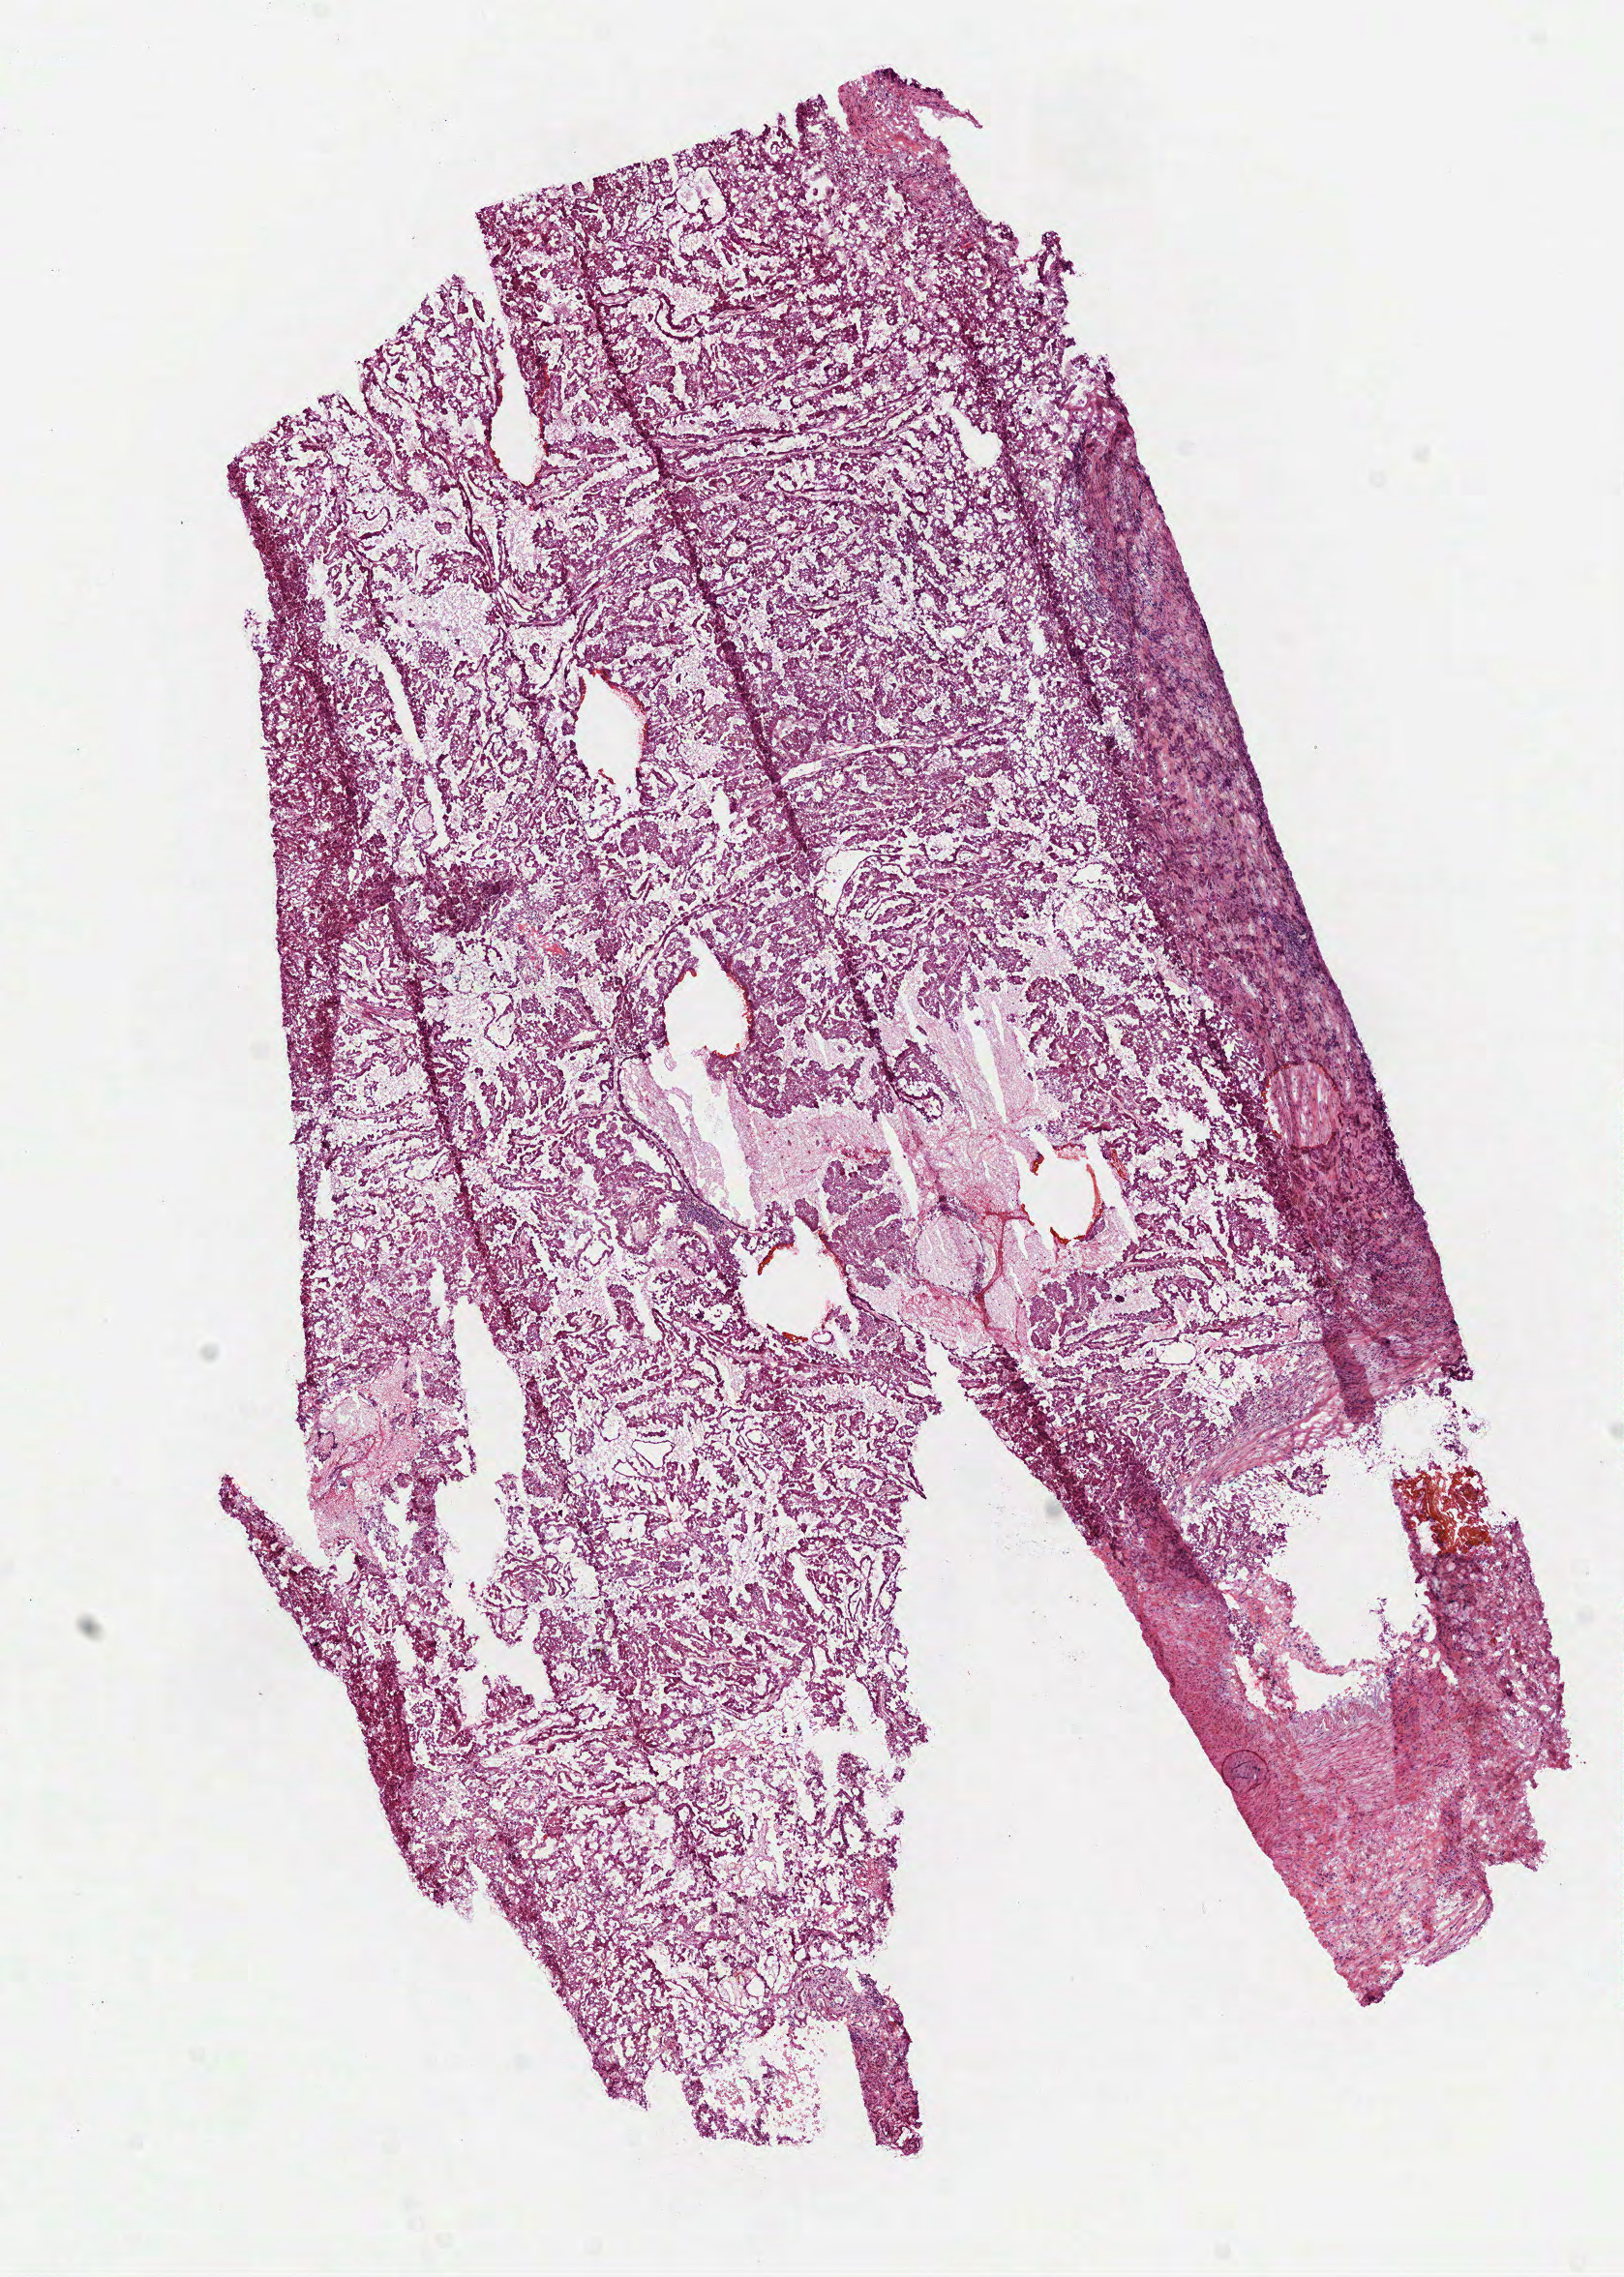
Digitized Hematoxylin and eosin (H&E) stained tissue section (whole slide), shown as a low-resolution overview of the whole scanned area (about 6.8 x 9.5 mm, acquisition: 40x scan). Frozen section. Sample: primary tumour, kidney. Male, age 67 years at initial diagnosis. Composition of this section per pathologist review: tumour nuclei 90%, necrosis 0%.
• AJCC pathologic stage: III (6th edition)
• pathologic diagnosis: Papillary adenocarcinoma, NOS
• laterality: left